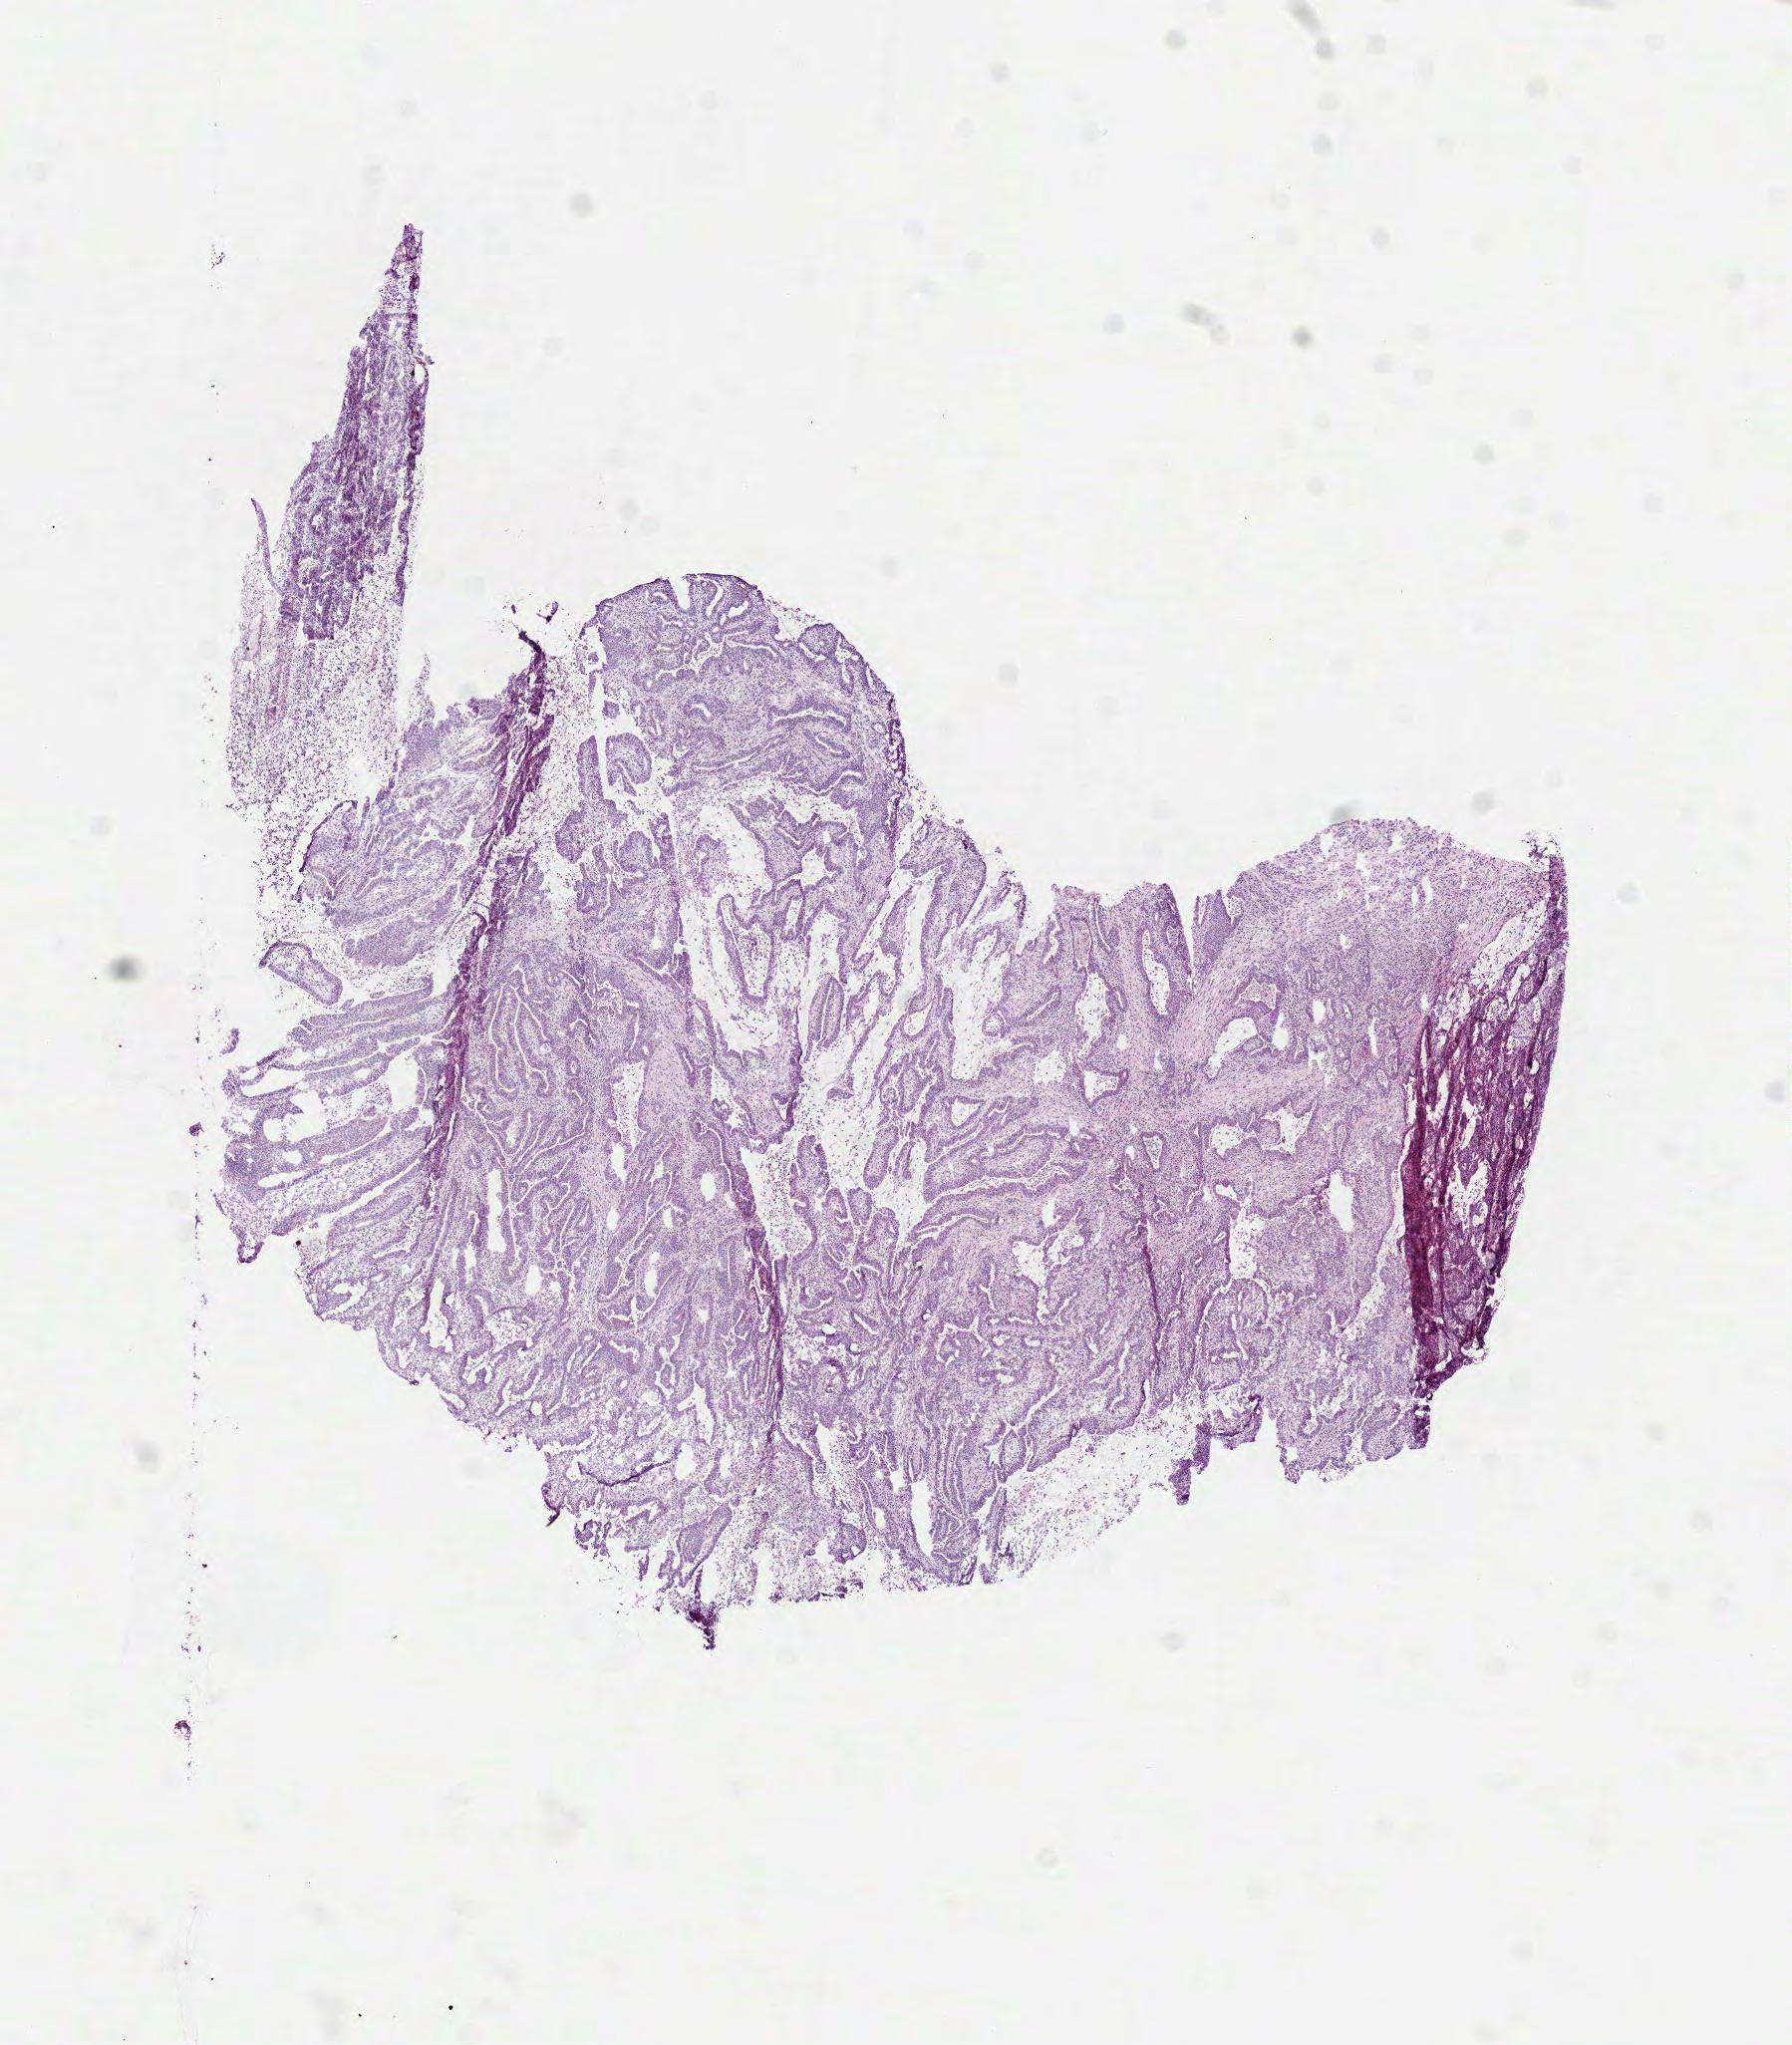
H&E-stained whole-slide image — low-resolution overview of the scanned area, about 7.3 x 8.3 mm (slide scanned at 40x). Frozen section from the top of the tissue portion. Primary tumour sample from the colon. Male, age 80 years at initial diagnosis. Composition of this section per pathologist review: tumour cells 65%, tumour nuclei 70%, normal cells 0%, stromal cells 33%, necrosis 2%. Infiltration values recorded for this section: lymphocyte infiltration 10%, monocyte infiltration 0%, neutrophil infiltration 3%.
Diagnosis: Mucinous adenocarcinoma (hepatic flexure of colon). Lymph nodes positive (case pathology): 0 of 18 examined. AJCC pathologic stage: IIA.